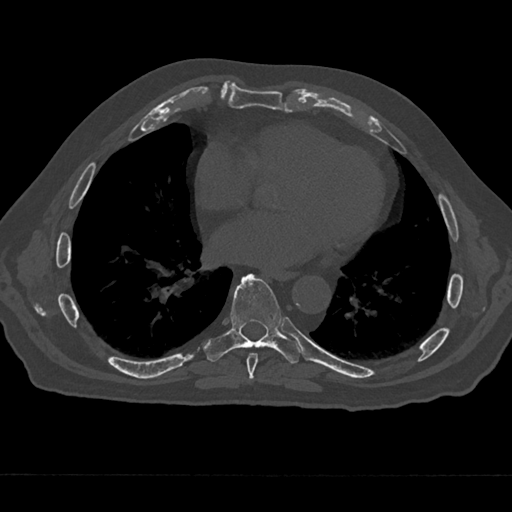
CT including the spine, one axial slice; position 332 of 797 along the scan axis; 120 kVp; bone window (W 1800 / L 400 HU); 0.5 mm slice thickness; 512 × 512 image matrix. Male patient, age 75 years. From the clinical record (not read from this slice): primary cancer: renal; vertebrae with lytic lesions (as recorded): T4.
Structures marked on this image (semi-automatic segmentation, software-assisted and operator-edited):
- T7 vertebra: box from (x=245, y=353) to (x=258, y=381) px
- T8 vertebra: (x=204, y=273)–(x=301, y=363)